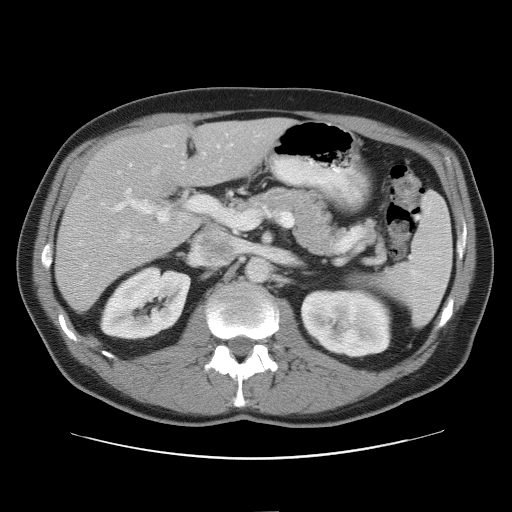
Contrast-enhanced abdominal CT, one axial slice. Slice 32 of 52 in the series (ordered by position). Reconstruction kernel STANDARD. Intravenous contrast given. Soft-tissue window (W 400 / L 40 HU). 512 × 512 image matrix, field of view 393 × 393 mm. Male patient, age 70 years. Case-level facts recorded for this patient, not image findings: diagnosis: colorectal cancer liver metastases, imaged before liver resection; multiple liver metastases: yes; largest metastasis: 4 cm; chemotherapy before resection: yes.
Annotated regions visible in this slice (outlined manually by an expert reader):
- hepatic veins: box from (x=75, y=167) to (x=159, y=268) px
- liver: (x=57, y=120)–(x=289, y=311)
- planned liver remnant (the part of the liver to remain after resection): (x=112, y=120)–(x=288, y=187)
- portal vein (with intrahepatic branches): (x=115, y=144)–(x=232, y=223)